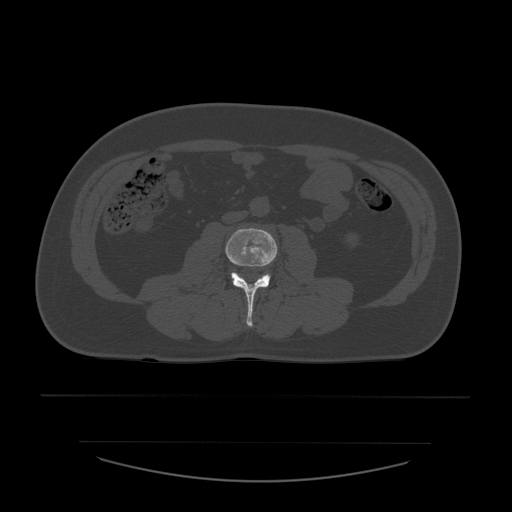
CT including the spine, one axial slice. Position 170 of 532 along the scan axis. 120 kVp. Bone window (W 1800 / L 400 HU). 512 × 512 image matrix, field of view 441 × 441 mm. Patient age 44 years. From the clinical record (not read from this slice): primary cancer: soft tissue sarcoma.
Annotated regions visible in this slice (semi-automatically segmented with operator editing):
- L3 vertebra: bounding box [x1, y1, x2, y2] px = [226, 229, 278, 327]